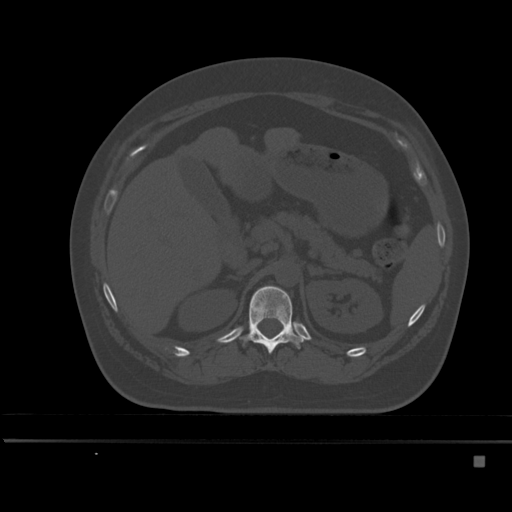
CT including the spine, one axial slice. Slice 213 of 495 in the series (ordered by position). Bone window (W 1800 / L 400 HU). 1.5 mm slice thickness. 512 × 512 image matrix. Patient: female, 33 years. From the clinical record (not read from this slice): primary cancer: breast.
Annotated regions visible in this slice (semi-automatically segmented with operator editing):
- T12 vertebra: bounding box (x1, y1, x2, y2) in pixels: (239, 286, 304, 353)